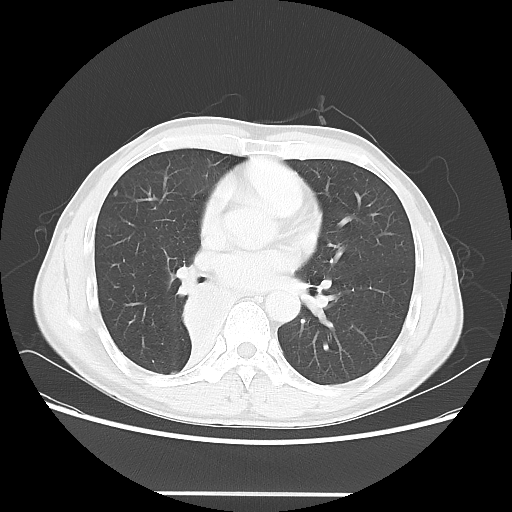
Chest CT, one axial slice. Position 31 of 62 along the scan axis. Reconstruction kernel LUNG. 120 kVp. Lung window (W 1500 / L -600 HU). 5 mm slice thickness. 512 × 512 image matrix, field of view 393 × 393 mm. Patient: male, 47 years. From the clinical record (not read from this slice): clinical TNM (as recorded): T2 N0 M0.
Structures marked on this image (bounding box drawn by a radiologist):
- lung tumour (recorded histology: squamous cell carcinoma): bounding box (x1, y1, x2, y2) in pixels: (176, 282, 237, 350)